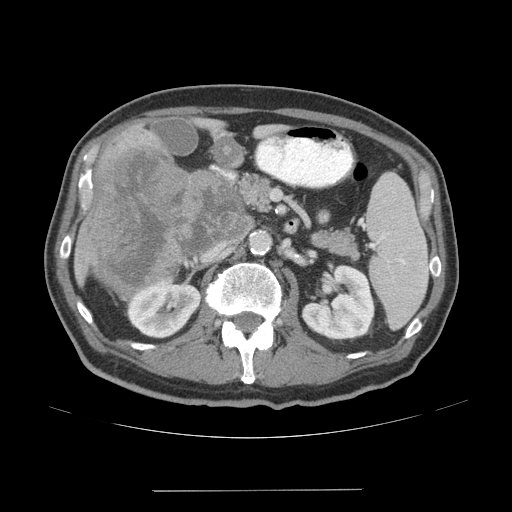
Contrast-enhanced abdominal CT (liver protocol), one axial slice; slice 18 of 77 in the series (ordered by position); reconstruction kernel STANDARD; soft-tissue window (W 400 / L 40 HU); 2.5 mm slice thickness; 512 × 512 image matrix, field of view 400 × 400 mm. Case-level facts recorded for this patient, not image findings: diagnosis: hepatocellular carcinoma (patient treated with transarterial chemoembolisation; whether this scan precedes or follows treatment is not stated here); TNM stage (as recorded): Stage-IVA; Child-Pugh class: A; tumour differentiation: well differentiated; tumour nodularity: uninodular.
Annotated regions visible in this slice (semi-automatic segmentation, software-assisted and operator-edited):
- liver parenchyma outside the tumour (the mass and vessels are separate outlines, so this box may not span the whole liver): box from (x=74, y=126) to (x=252, y=302) px
- mass: (x=88, y=143)–(x=241, y=296)